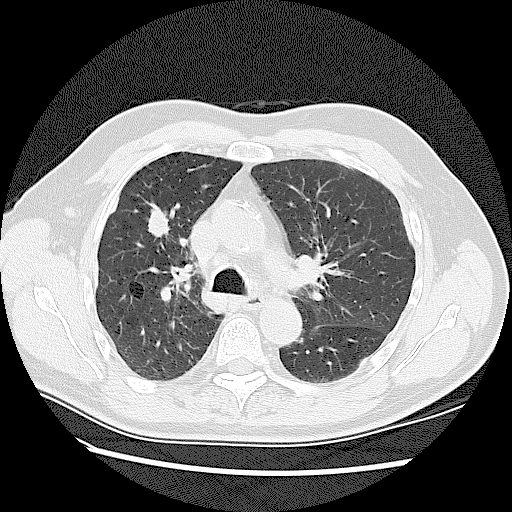
Low-dose screening chest CT, one axial slice; slice 84 of 128 in the series (ordered by position); reconstruction kernel LUNG; 120 kVp; lung window (W 1500 / L -600 HU); 2.5 mm slice thickness; 512 × 512 image matrix, field of view 360 × 360 mm.
Annotated regions visible in this slice (outlined manually by an expert reader):
- lesion 1 (tumor, upper lobe of right lung): bounding box [x1, y1, x2, y2] px = [148, 209, 170, 238]